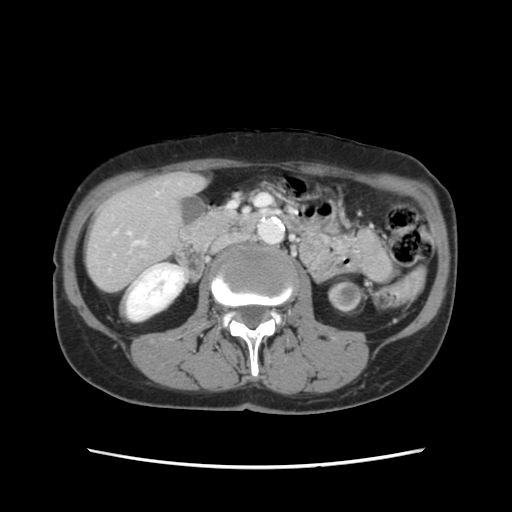
Contrast-enhanced abdominal CT, one axial slice; position 35 of 120 along the scan axis; soft-tissue window (W 400 / L 40 HU); 512 × 512 image matrix, field of view 330 × 330 mm. Female patient, age 70 years. From the clinical record (not read from this slice): diagnosis: colorectal cancer liver metastases, imaged before liver resection.
Outlined on this slice (manually delineated by an expert):
- hepatic veins: bounding box <136,242,139,244> (left, top, right, bottom; pixels)
- liver: <86,176,201,290>
- planned liver remnant (the part of the liver to remain after resection): <86,175,202,291>
- portal vein (with intrahepatic branches): <128,232,131,236>